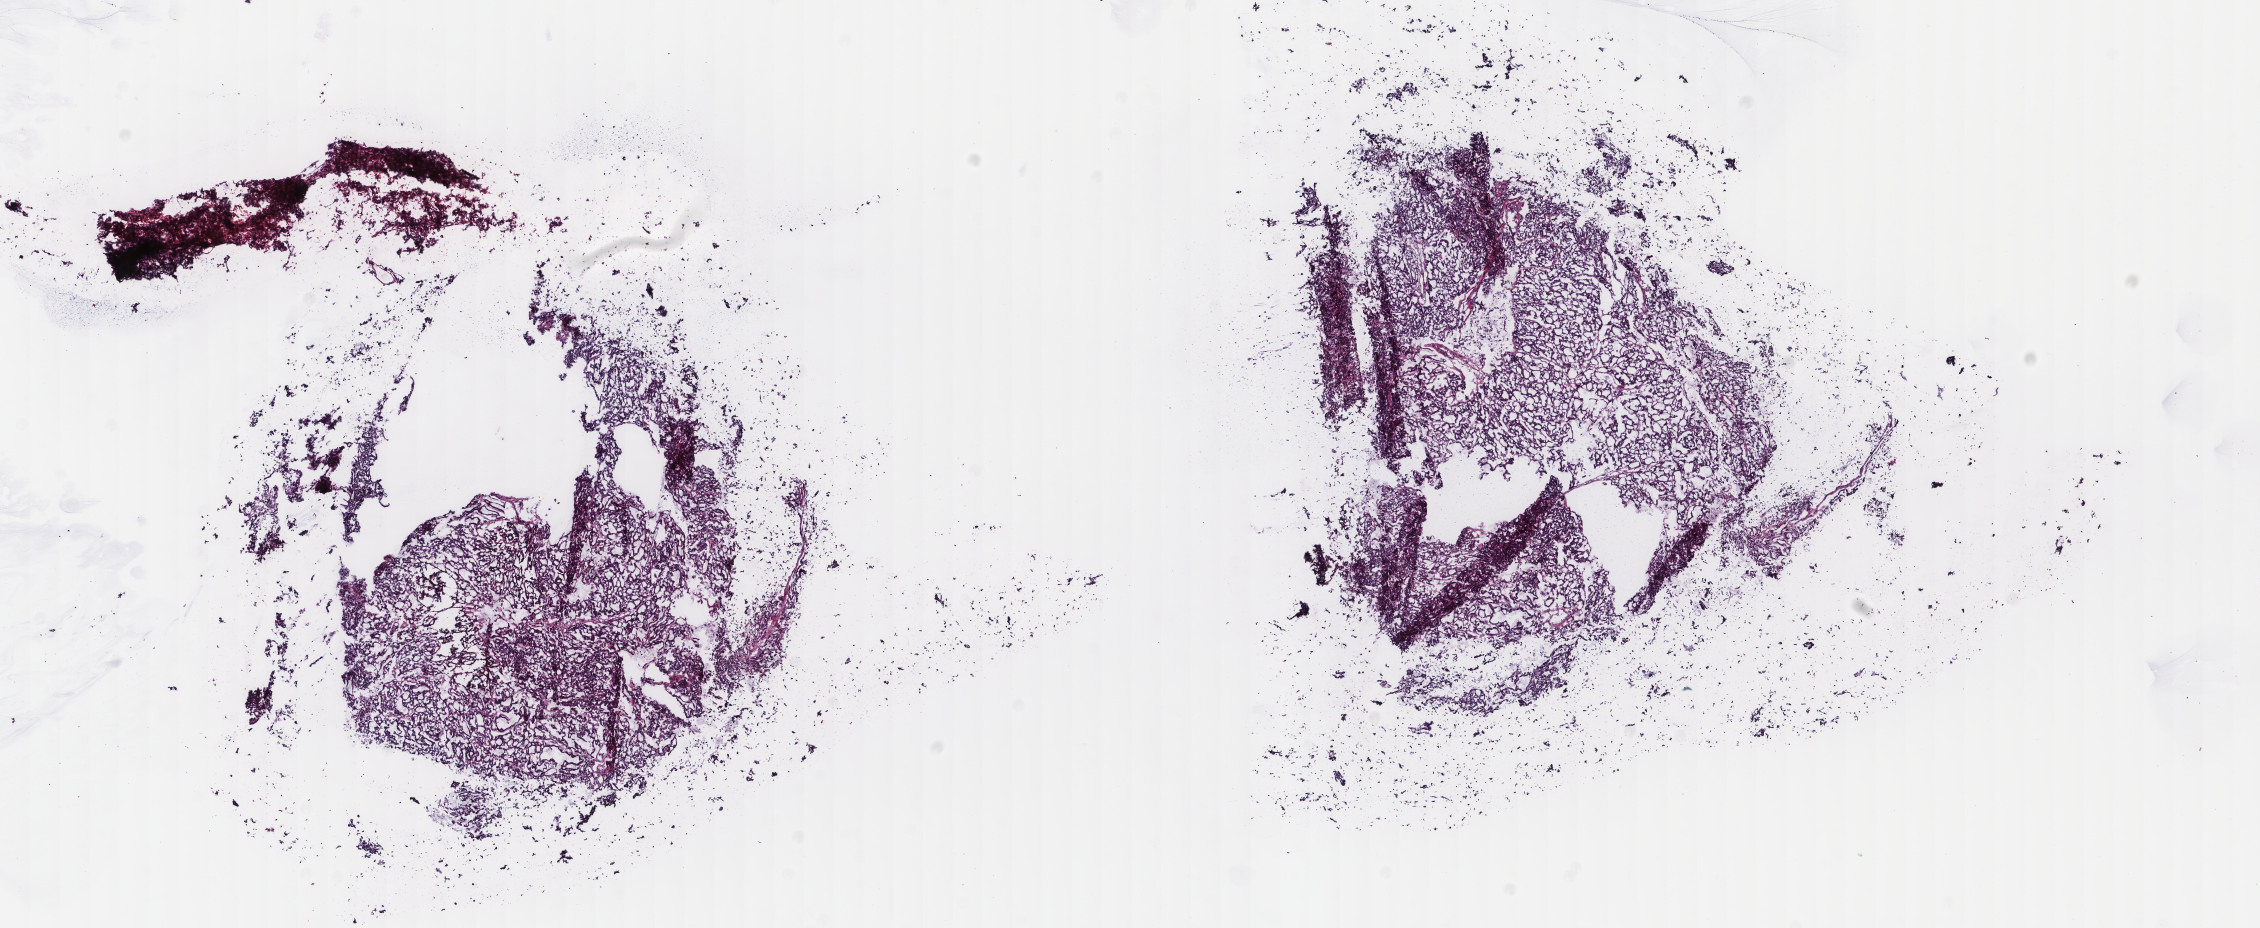
Whole-slide histology image, H&E-stained — whole scanned area (about 17.9 x 7.4 mm) shown as a low-resolution overview. Frozen section. Primary tumour sample from the uterus. Patient: female, age at initial diagnosis 60 years. Histologic grade: G3 (poorly differentiated). Composition of this section per pathologist review: tumour cells 90%, tumour nuclei 90%, normal cells 0%, stromal cells 5%, necrosis 5%. Inflammatory infiltration, as recorded: lymphocyte infiltration 20%, monocyte infiltration 20%, neutrophil infiltration 40%.
* lymph nodes positive (case pathology): 0 of 11 examined
* FIGO stage: IIIA
* diagnosis: Serous cystadenocarcinoma, NOS (endometrium)